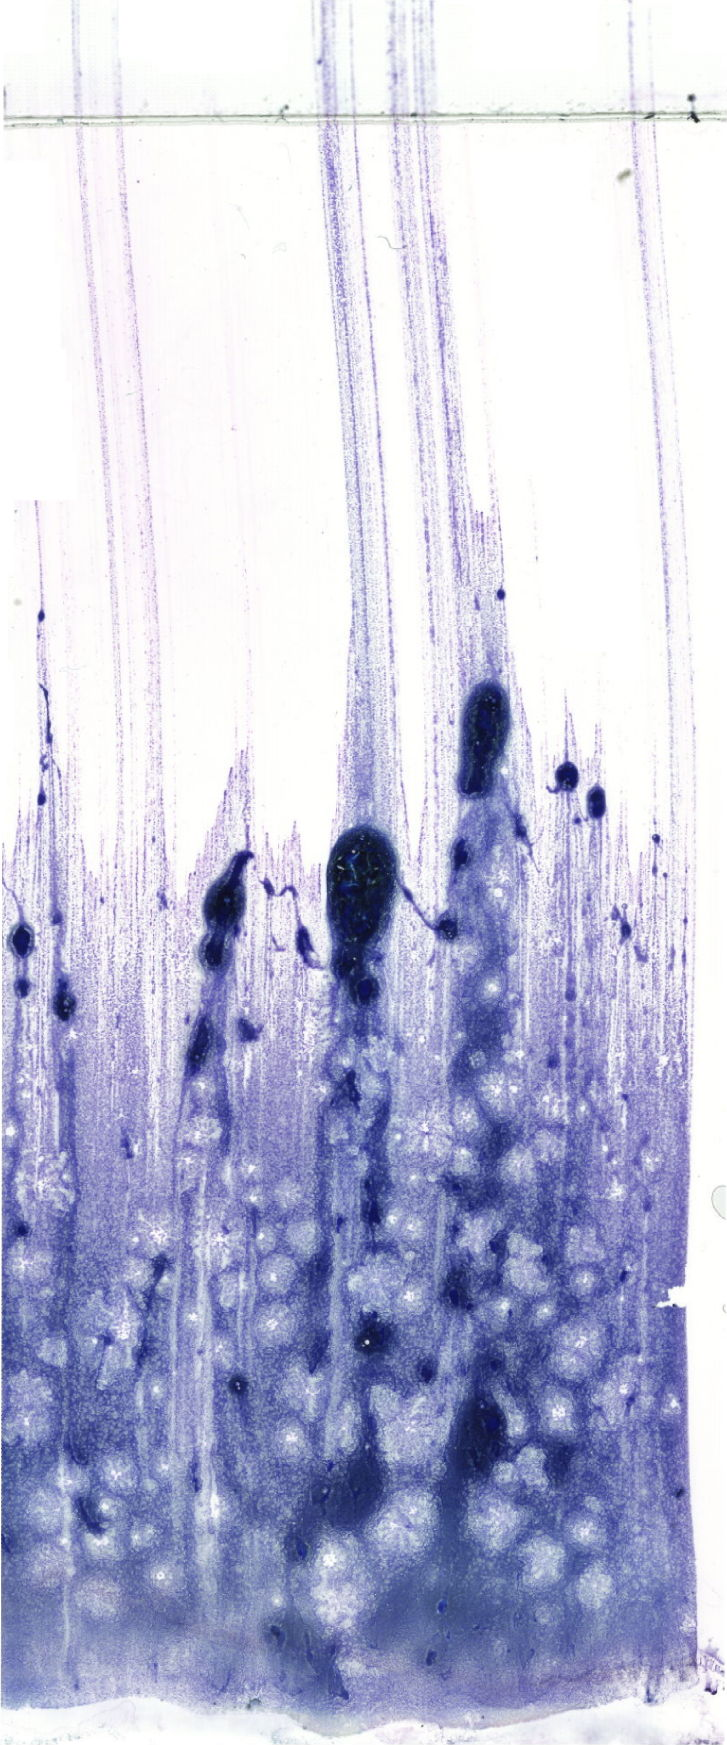
May-Grünwald-Giemsa (MGG)-stained marrow aspirate smear (whole slide), whole scanned area (about 20.6 x 49.5 mm) shown as a low-resolution overview. Patient sex: male.
Diagnosis: Acute Monocytic Leukemia.